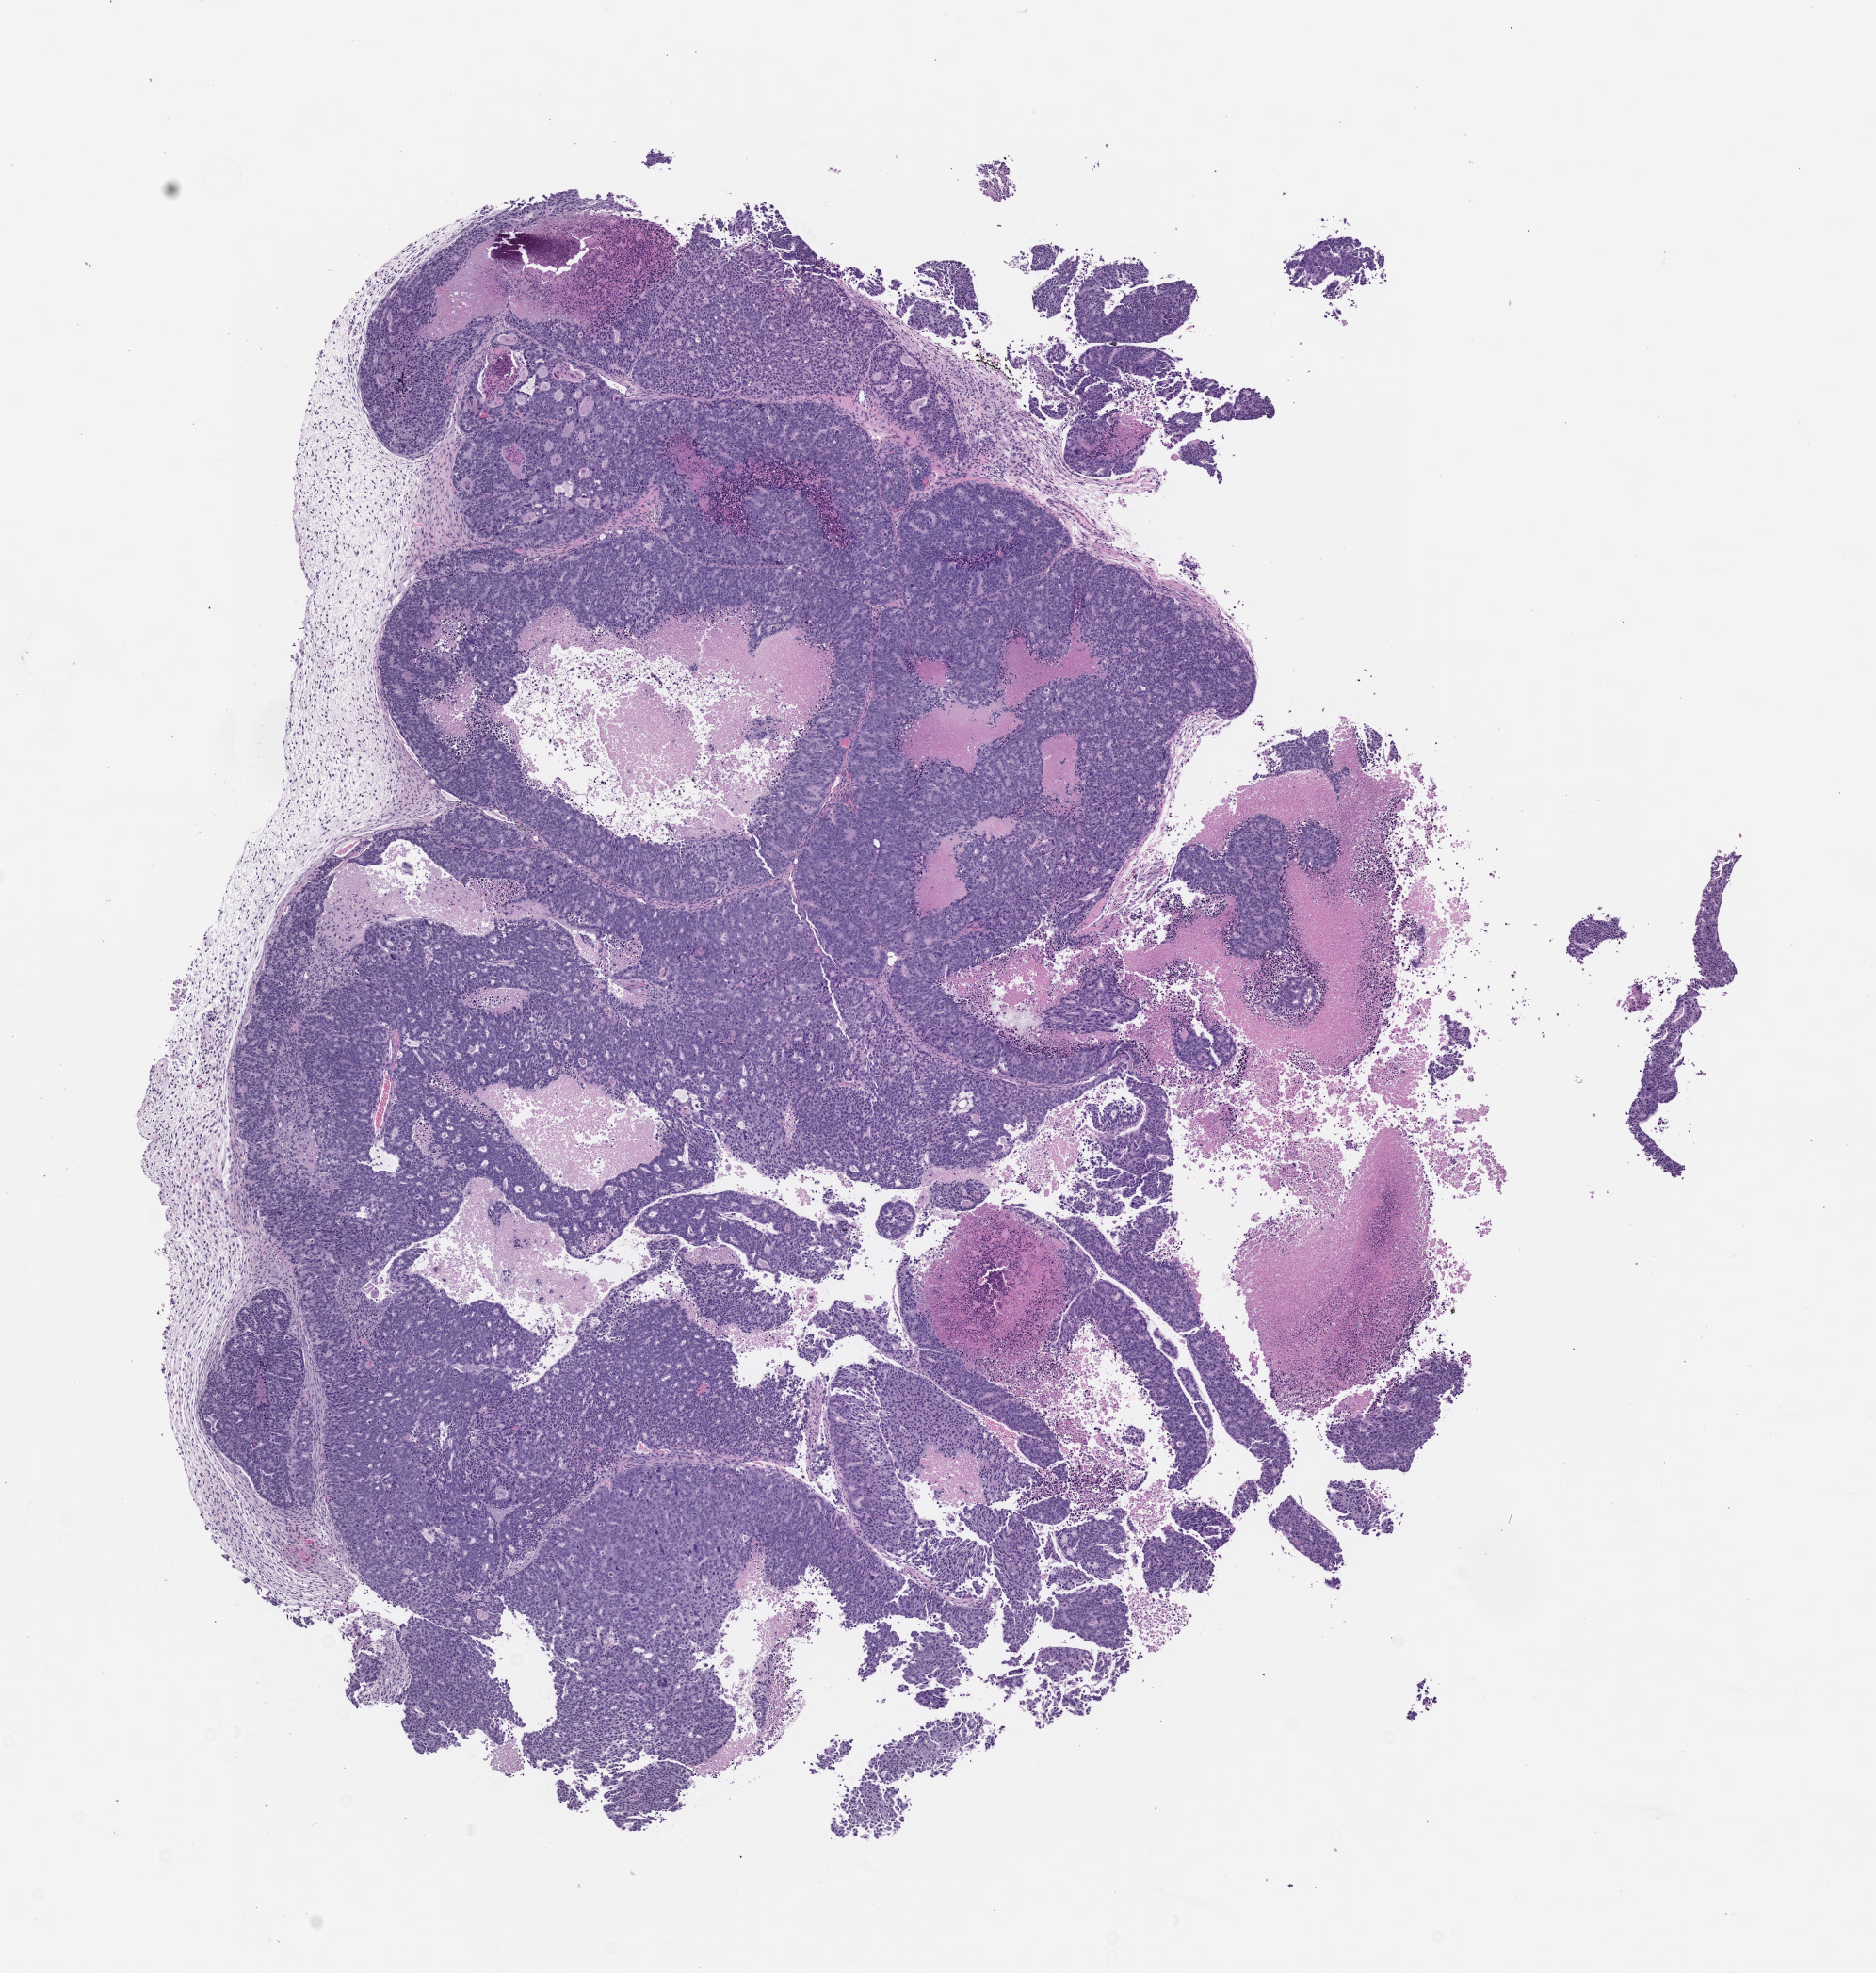
Whole-slide image, hematoxylin and eosin (H&E): patient-derived xenograft (human tumor grown in a mouse), passage 1 — a low-resolution overview of the entire scanned area, about 8.0 x 8.4 mm; FFPE section; originating tumor site category: colon.
Originating patient diagnosis: Colon Adenocarcinoma.